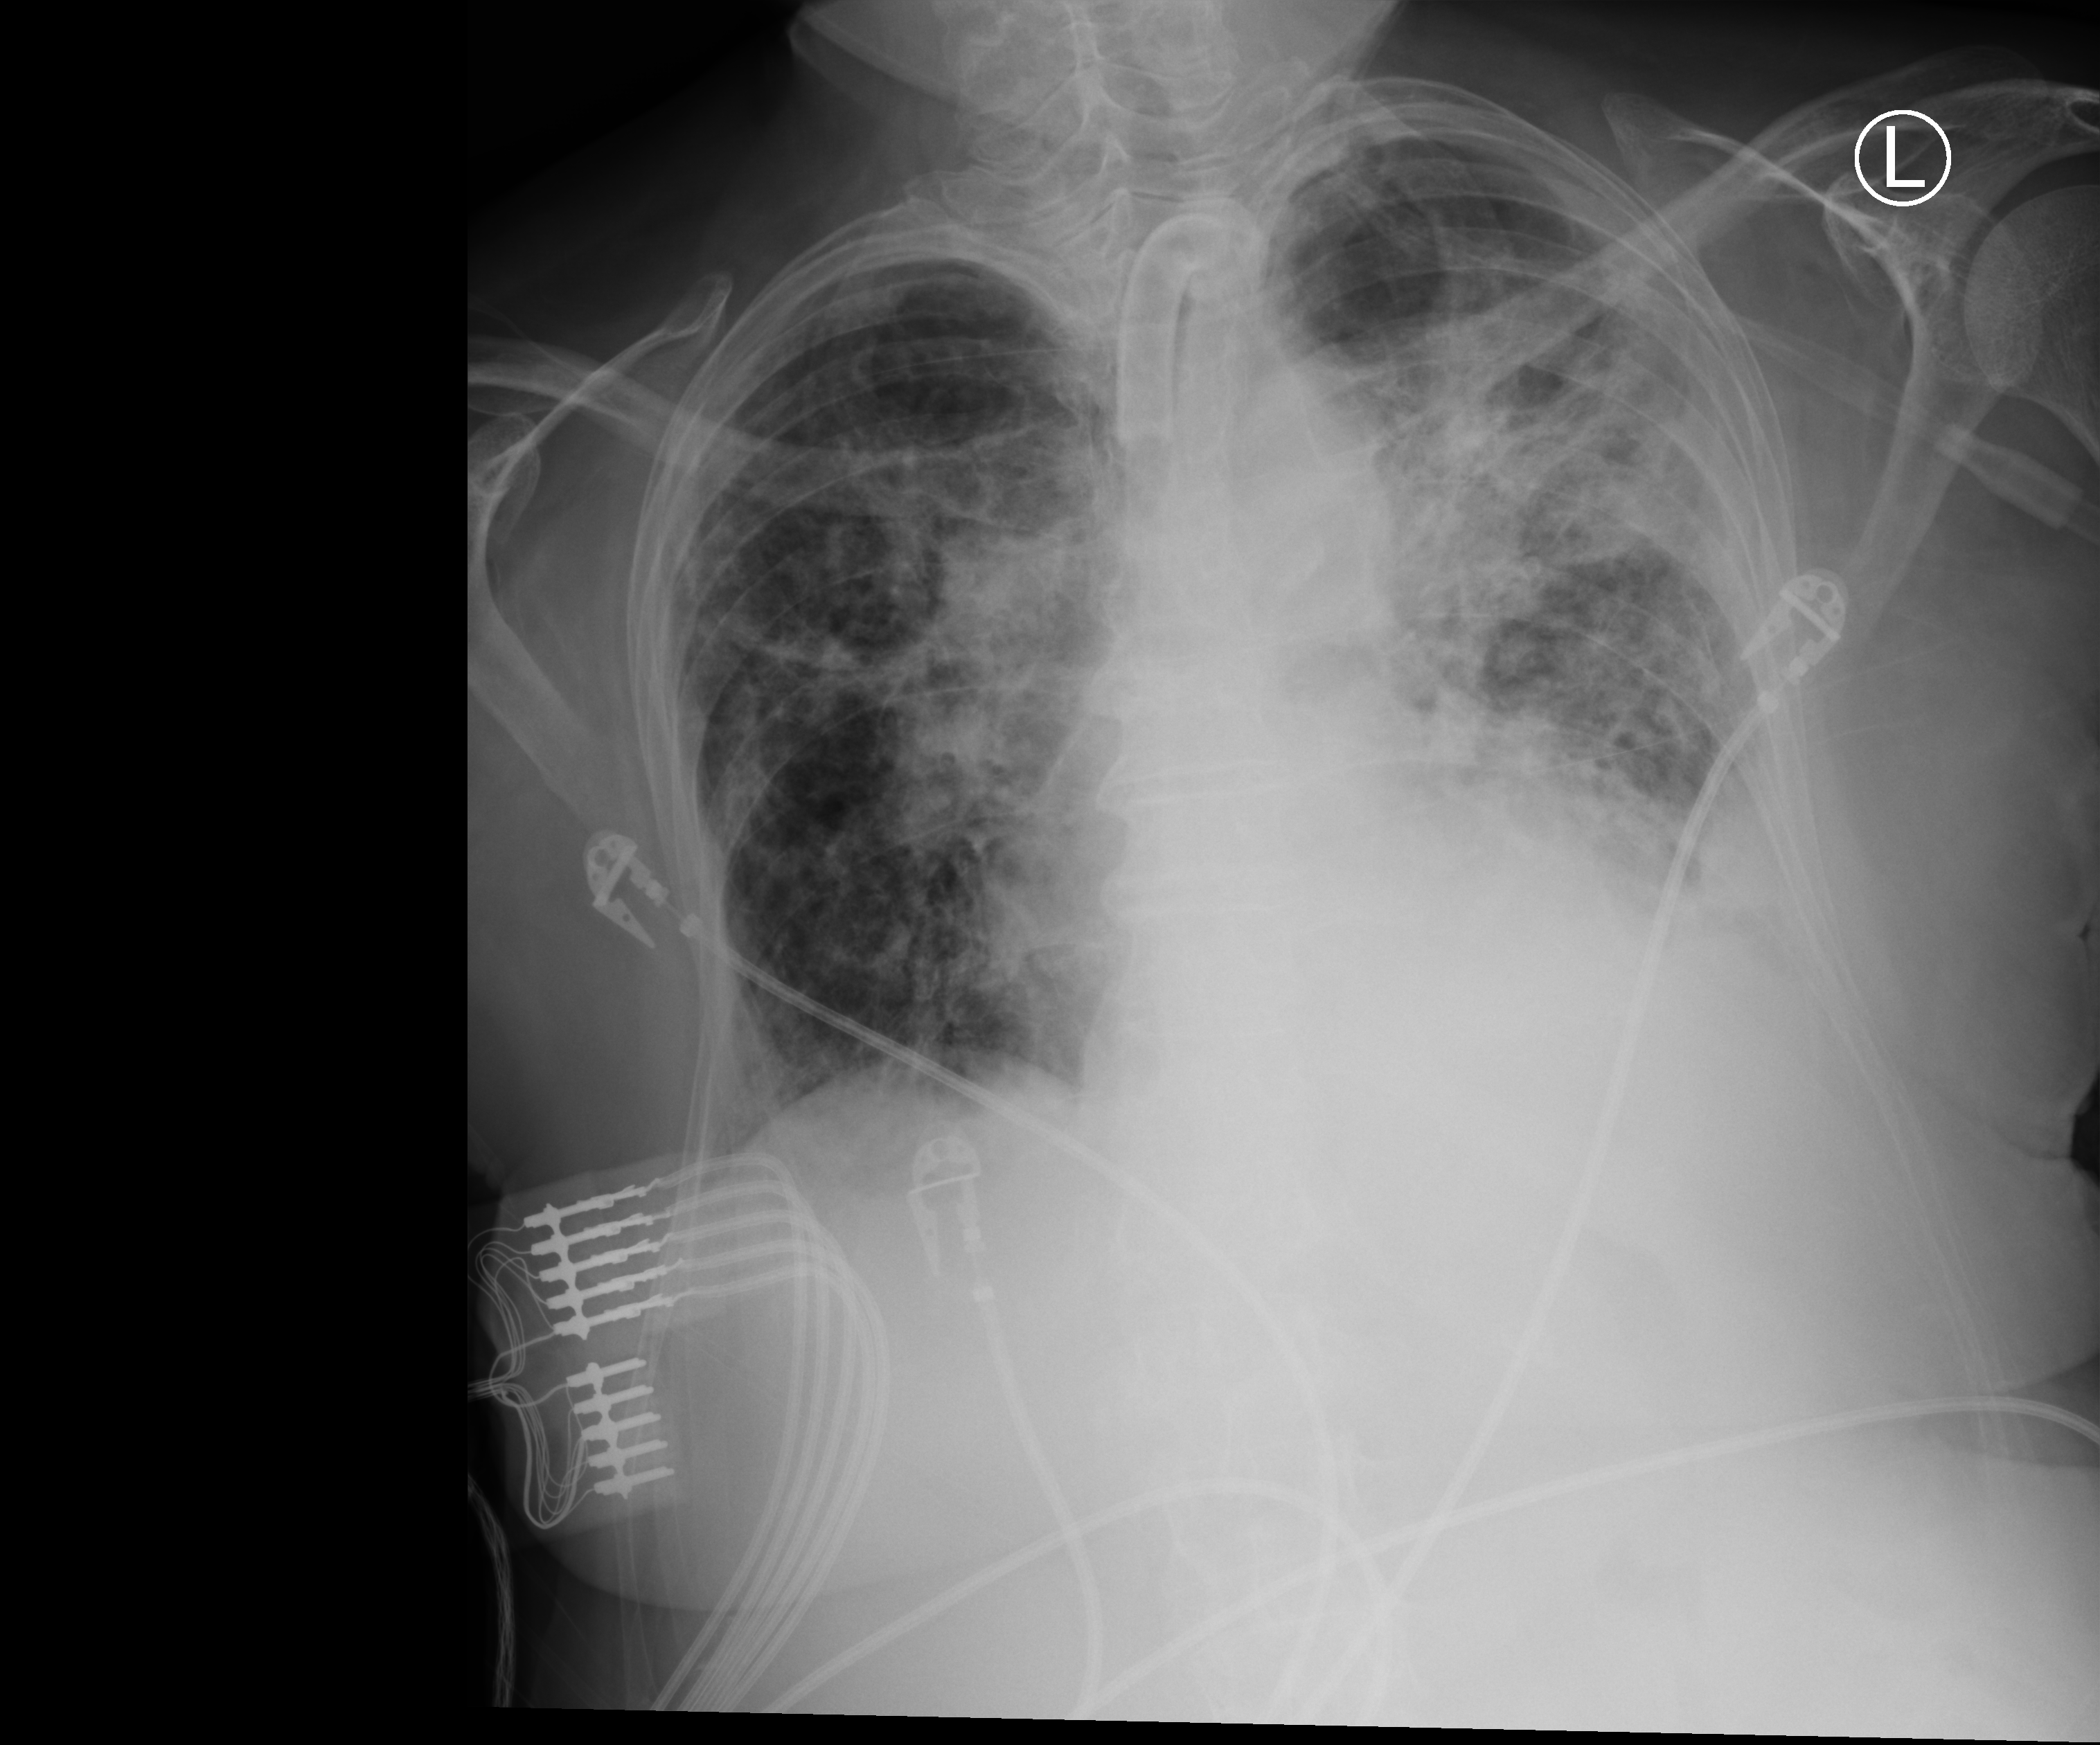
Bedside chest radiograph (computed radiography). Female patient hospitalised with COVID-19, age 75–90 years.
Admission-level facts for this patient (not findings on this image; timing relative to this image not recorded): chronic kidney disease (admission record): no; COPD (admission record): no; mechanically ventilated during this hospital stay: yes.